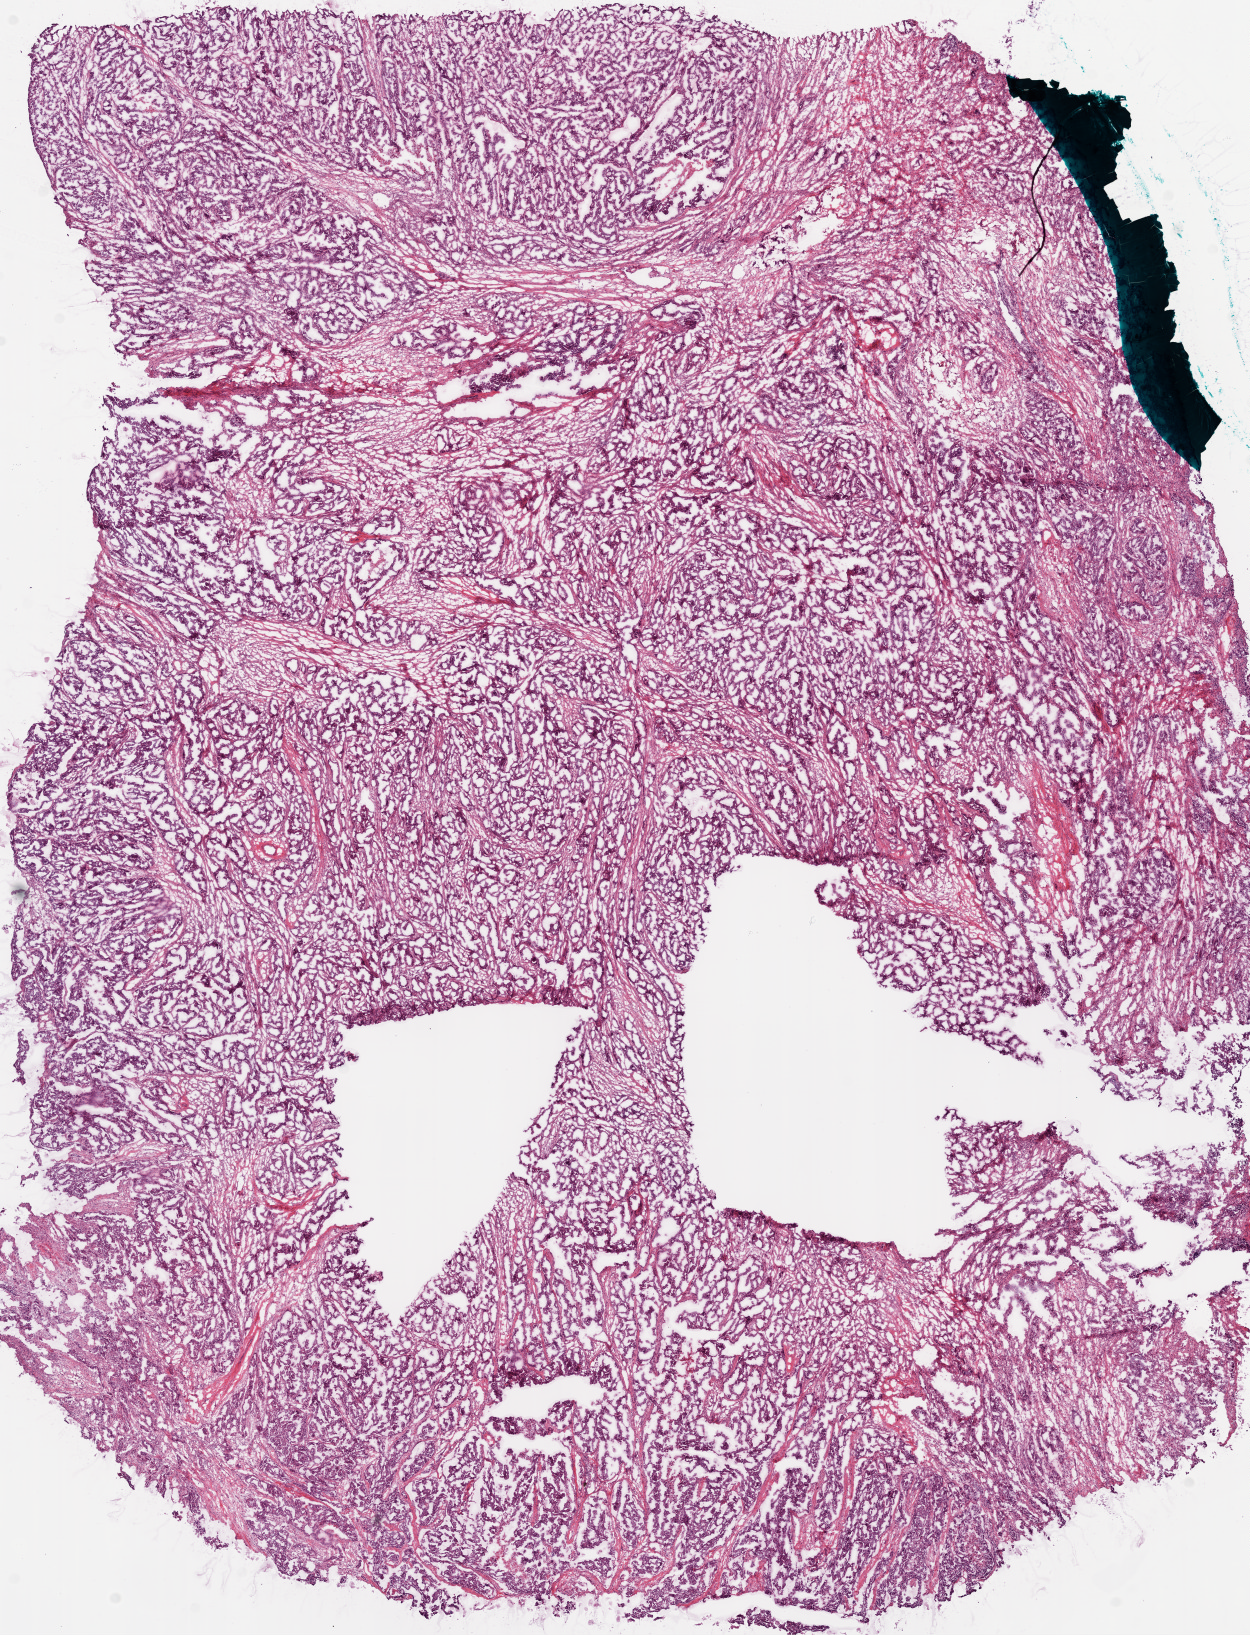
Whole-slide histology image, Hematoxylin and eosin (H&E) stained, shown as a low-resolution overview of the whole scanned area (about 10.0 x 13.1 mm, slide scanned at 20x); frozen section from the bottom of the tissue portion; ovary, primary tumour sample. Patient: female, age at initial diagnosis 39 years. Histologic grade: G3 (poorly differentiated). Slide review estimates, as recorded: tumour cells 89%, tumour nuclei 90%, normal cells 0%, stromal cells 10%, necrosis 1%.
• FIGO stage: IIIC
• diagnosis: Serous cystadenocarcinoma, NOS